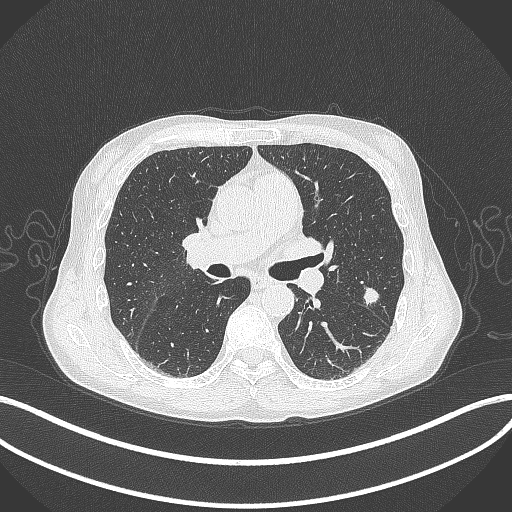
Chest CT, one axial slice. Position 208 of 429 along the scan axis. Reconstruction kernel B70f. Lung window (W 1500 / L -600 HU). 512 × 512 image matrix. Patient: male, 58 years. From the clinical record (not read from this slice): clinical TNM (as recorded): T1c N0 M0.
Annotated regions visible in this slice (bounding box drawn by a radiologist):
- lung tumour (recorded histology: adenocarcinoma): bounding box (x1, y1, x2, y2) in pixels: (358, 285, 382, 307)